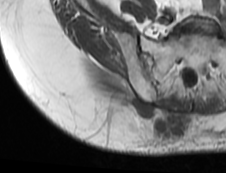
MRI of an extremity soft-tissue mass, one axial slice. MR volume resampled by the dataset authors to the PET/CT grid (not the native acquisition matrix). 3.27 mm slice thickness. 226 × 173 image matrix. Female patient. Case-level facts recorded for this patient, not image findings: histological type: spindle cell suggestive of myxofibrosarcoma; grade: intermediate; site of the primary tumour: right buttock.
Structures marked on this image (expert contour drawn on MRI and transferred to this co-registered scan by the dataset authors):
- gross tumour volume (mass): bounding box [x1, y1, x2, y2] px = [116, 95, 187, 139]